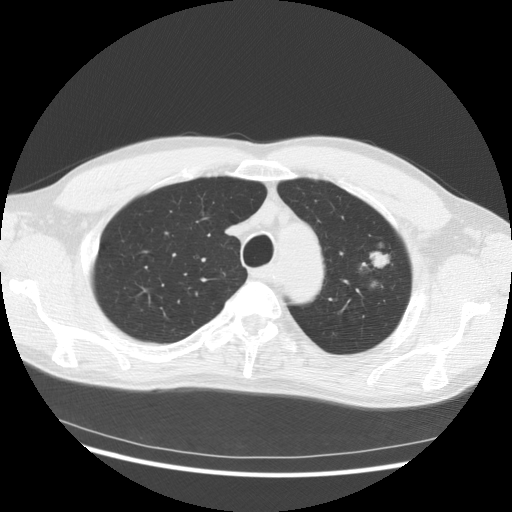
Axial slice from a low-dose chest CT screening exam; third screening round (two years after baseline); lung window (W 1500 / L -600 HU); standard (soft-tissue) reconstruction kernel (STANDARD); slice 112 of 145 in the series; 512 × 512 image matrix. Male participant, aged 61 years at enrolment. Former smoker at enrolment.
Expert-annotated lung lesion, box from (x=331, y=239) to (x=404, y=319) px. Screening reader's record for this exam (one nodule recorded; not confirmed to be the boxed lesion): non-calcified nodule or mass ≥4 mm, left upper lobe, 37 × 33 mm, poorly defined margins, mixed attenuation, pre-existing on the prior screen: yes; interval growth: yes. Official screen result: positive, other. Participant outcome: lung cancer diagnosed 361 days after this screen — bronchiolo-alveolar adenocarcinoma, NOS, left upper lobe, well differentiated (G1), stage IB (AJCC 6th edition), 44 mm at pathology.